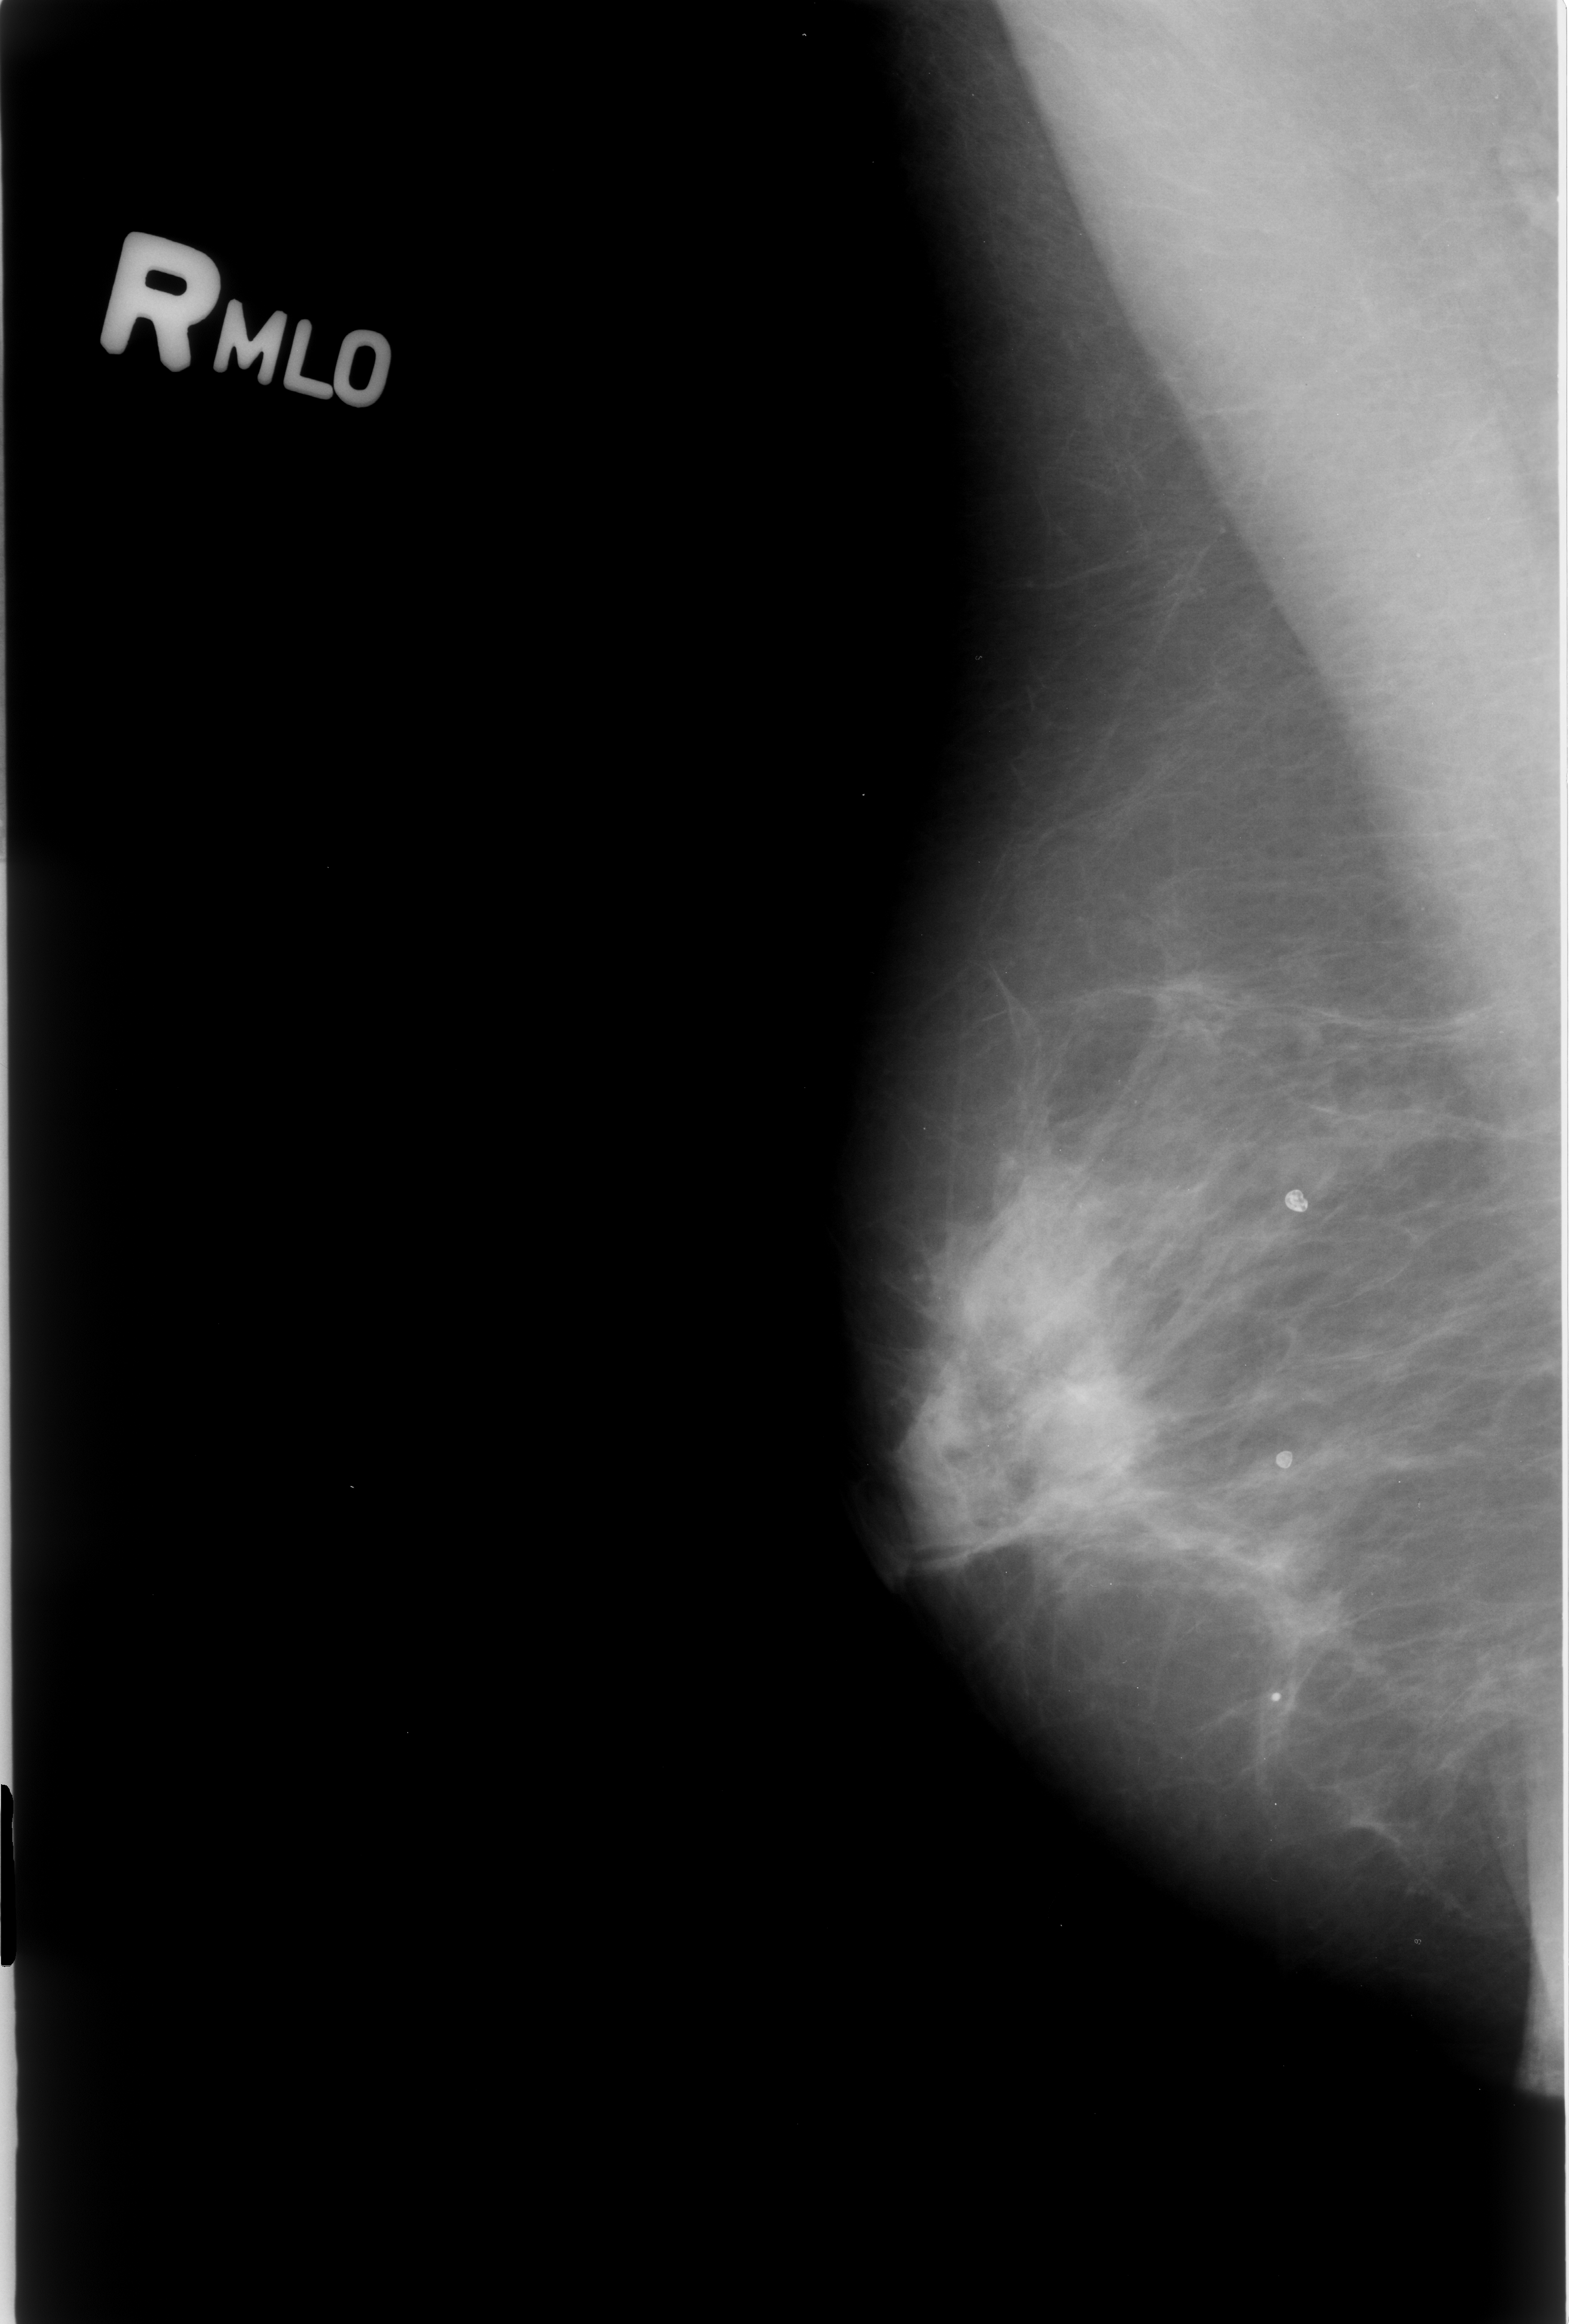
Scanned film-screen mammogram; right breast; mediolateral oblique (MLO) view; 1569 × 2324 image matrix.
Marked abnormalities (boxes around the expert regions of interest):
- mass, shape irregular, margins obscured / ill defined; BI-RADS assessment category 3; pathology result (as recorded, not read from the image): malignant: bounding box (x1, y1, x2, y2) in pixels: (1017, 1372, 1152, 1499)